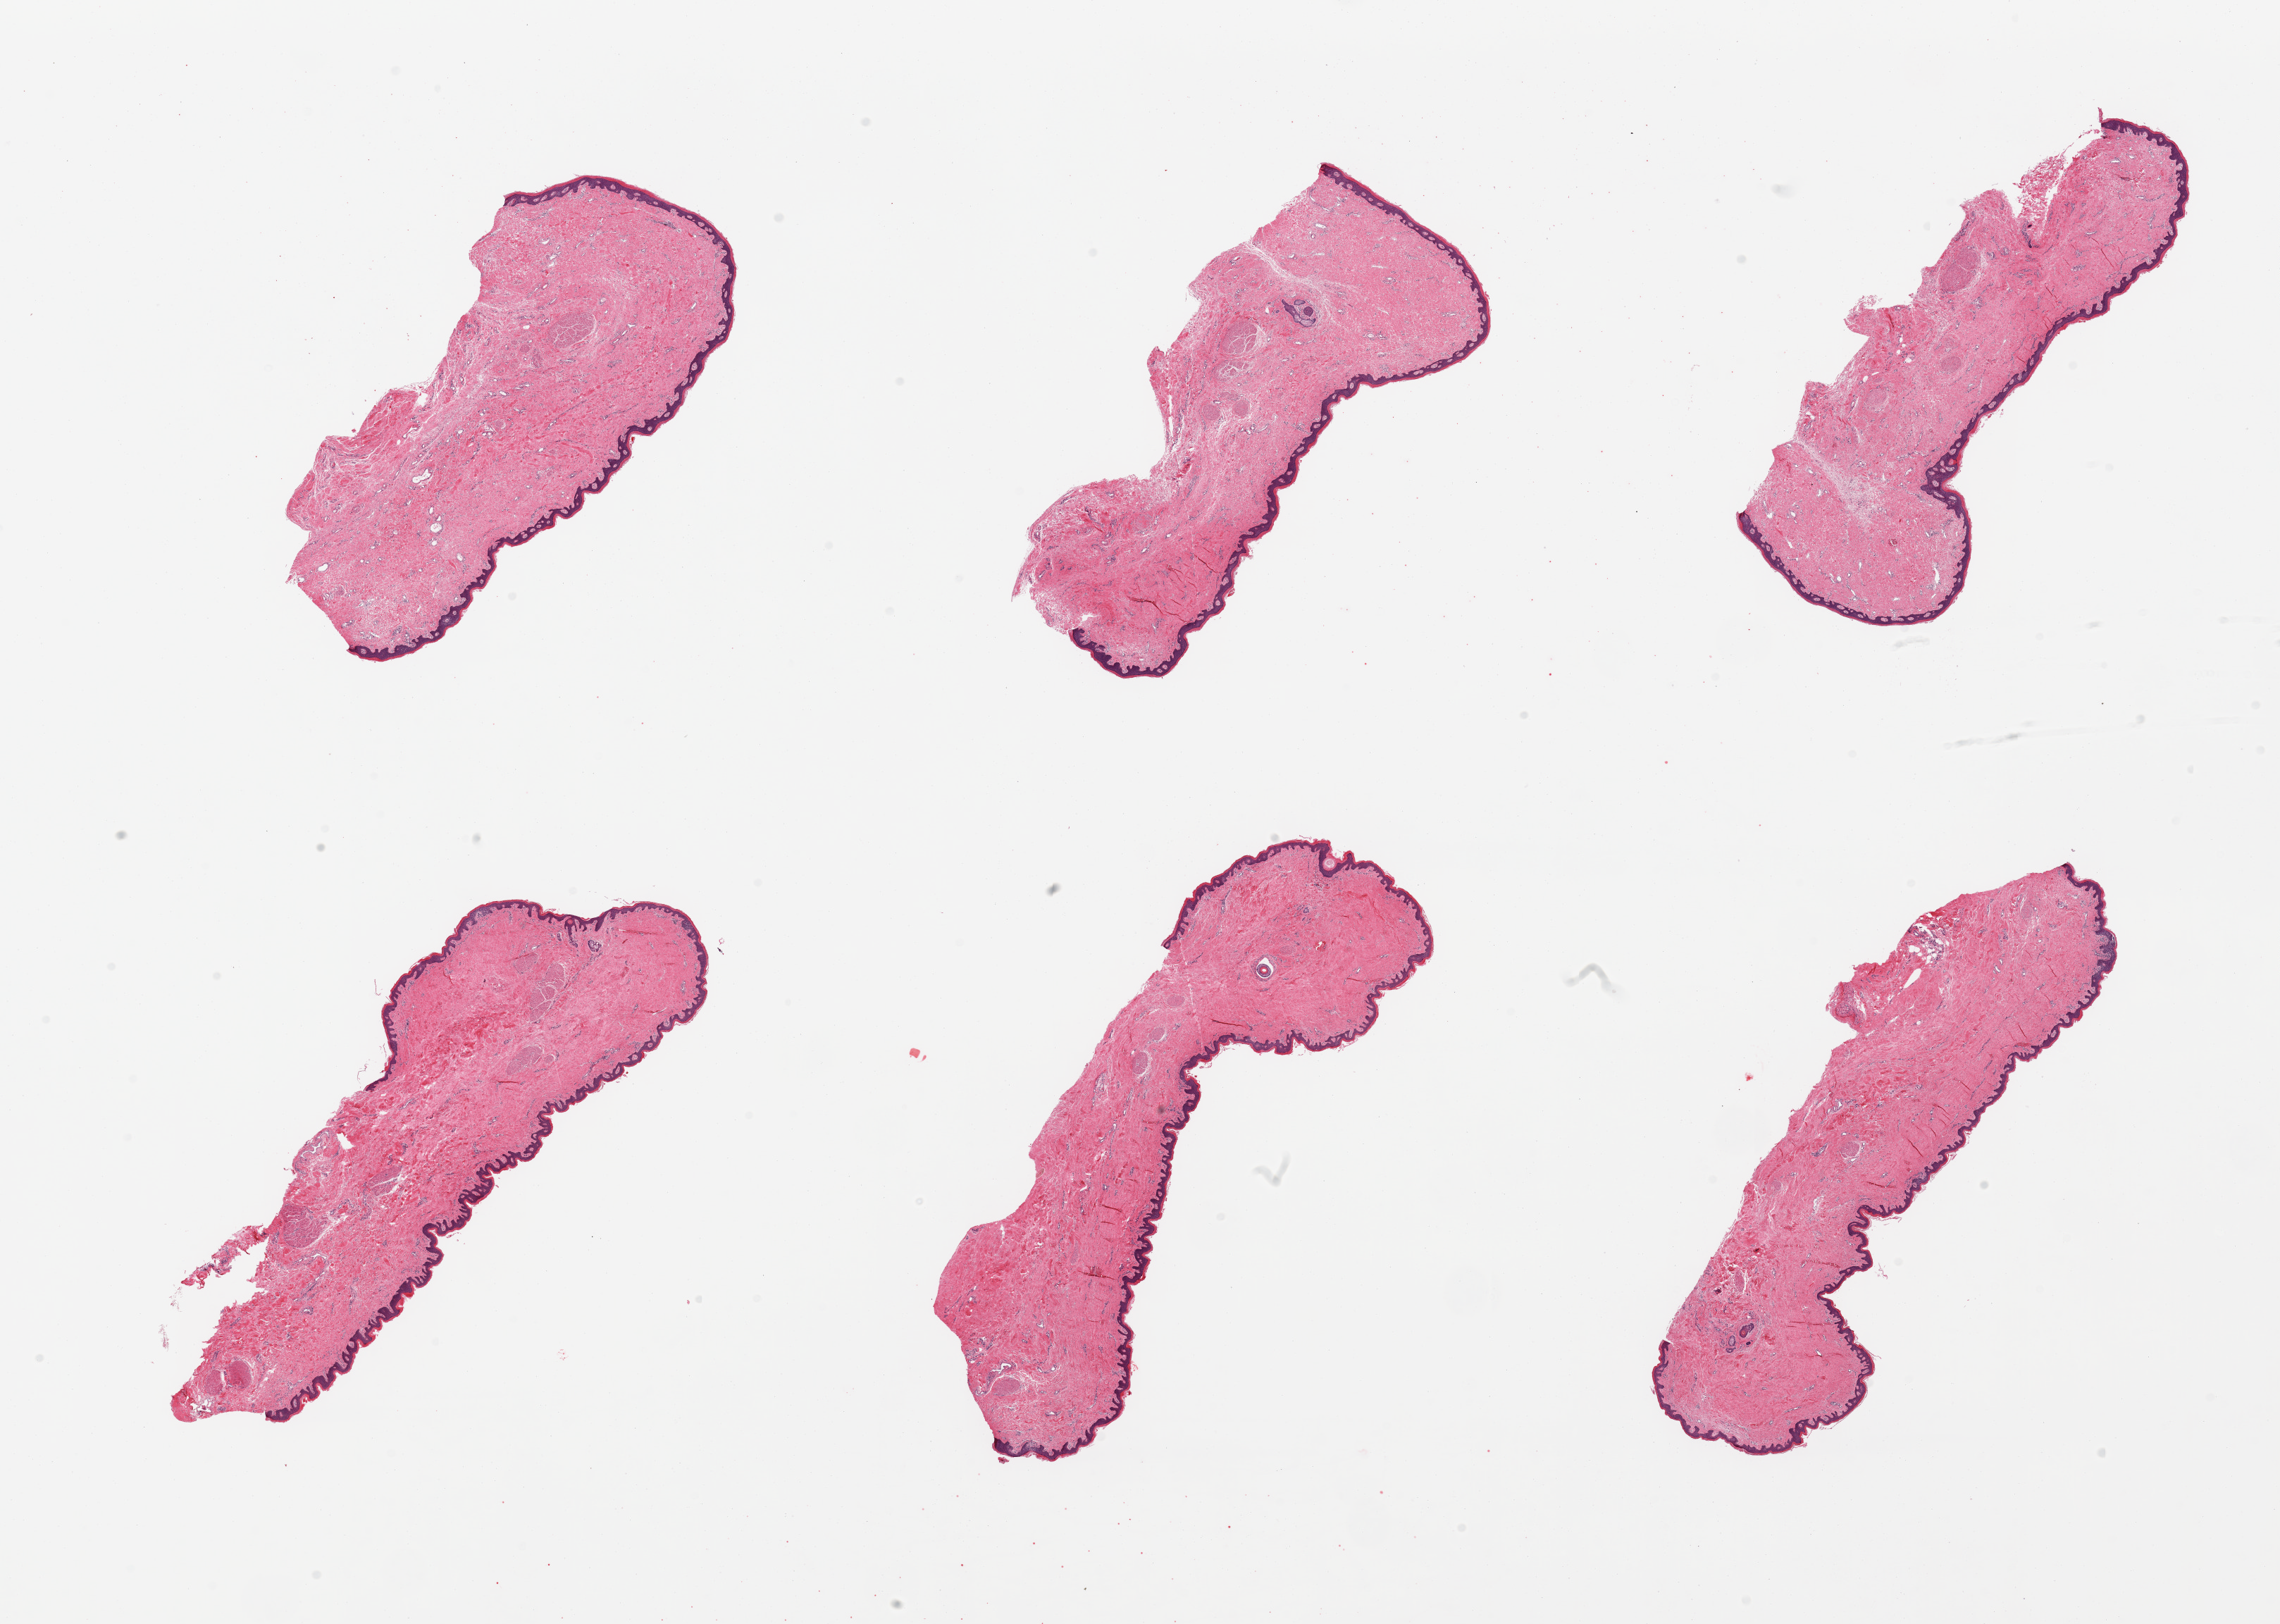
Hematoxylin and eosin (H&E) whole-slide image, whole scanned area (about 25.6 x 18.2 mm) shown as a low-resolution overview; PAXgene-fixed, paraffin-embedded tissue; sampled site (target tissue): skin of suprapubic region; tissue donor sample.
- reviewer comment on this tissue sample: 6 pieces; well trimmed